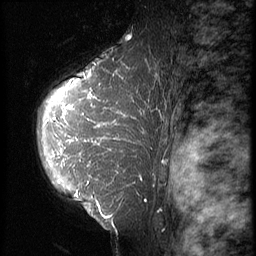
Breast MRI (dynamic contrast-enhanced), one sagittal slice; position 45 of 64 along the scan axis; 3 images stored at this slice position (order not interpretable as contrast timing); 1.5 T; TE 4.2 ms, TR 9 ms; 2.5 mm slice thickness; 256 × 256 image matrix. Patient: female, 39 years. Case-level facts recorded for this patient, not image findings: setting: breast cancer imaged before/during neoadjuvant chemotherapy; receptor status: HER2-positive.
Outlined on this slice (semi-automatically segmented with operator editing):
- analysis volume of interest (the breast-tissue region the enhancement analysis was run in; not a lesion): bounding box (x1, y1, x2, y2) in pixels: (32, 47, 151, 239)
- tumour enhancement mask (voxels above the 140 % enhancement threshold inside the analysis volume of interest): (51, 64, 145, 218)